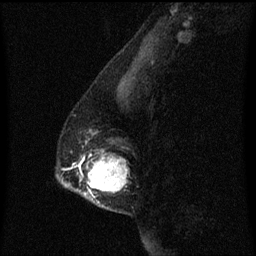
Breast MRI (dynamic contrast-enhanced), one sagittal slice. Position 21 of 60 along the scan axis. Dynamic contrast-enhanced series, image 2 of 3 at this slice position (ordered by acquisition). 1.5 T. TE 4.2 ms, TR 8.4 ms. 2 mm slice thickness. 256 × 256 image matrix, field of view 200 × 200 mm. Patient: female, 40 years. Case-level facts recorded for this patient, not image findings: setting: breast cancer imaged before/during neoadjuvant chemotherapy; receptor status: triple-negative.
Annotated regions visible in this slice (semi-automatic segmentation, software-assisted and operator-edited):
- analysis volume of interest (the breast-tissue region the enhancement analysis was run in; not a lesion): box from (x=60, y=140) to (x=129, y=211) px
- tumour enhancement mask (voxels above the 70 % enhancement threshold inside the analysis volume of interest): (x=82, y=156)–(x=129, y=195)